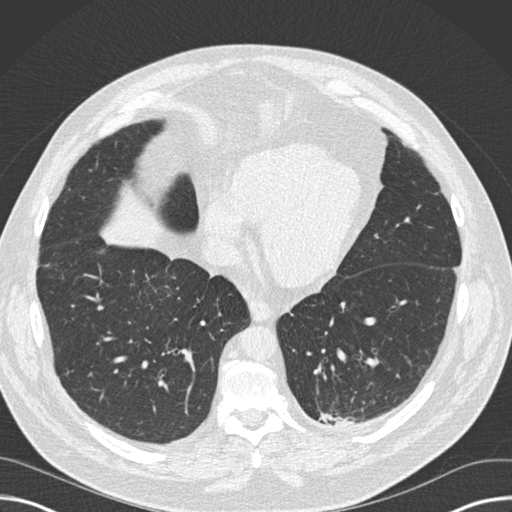
Low-dose screening chest CT, one axial slice; slice 53 of 160 in the series (ordered by position); reconstruction kernel B30f; 120 kVp; lung window (W 1500 / L -600 HU); 2 mm slice thickness; 512 × 512 image matrix, field of view 382 × 382 mm.
Structures marked on this image (manually delineated by an expert):
- lesion 1 (tumor, upper lobe of left lung): bounding box [x1, y1, x2, y2] px = [320, 414, 347, 424]